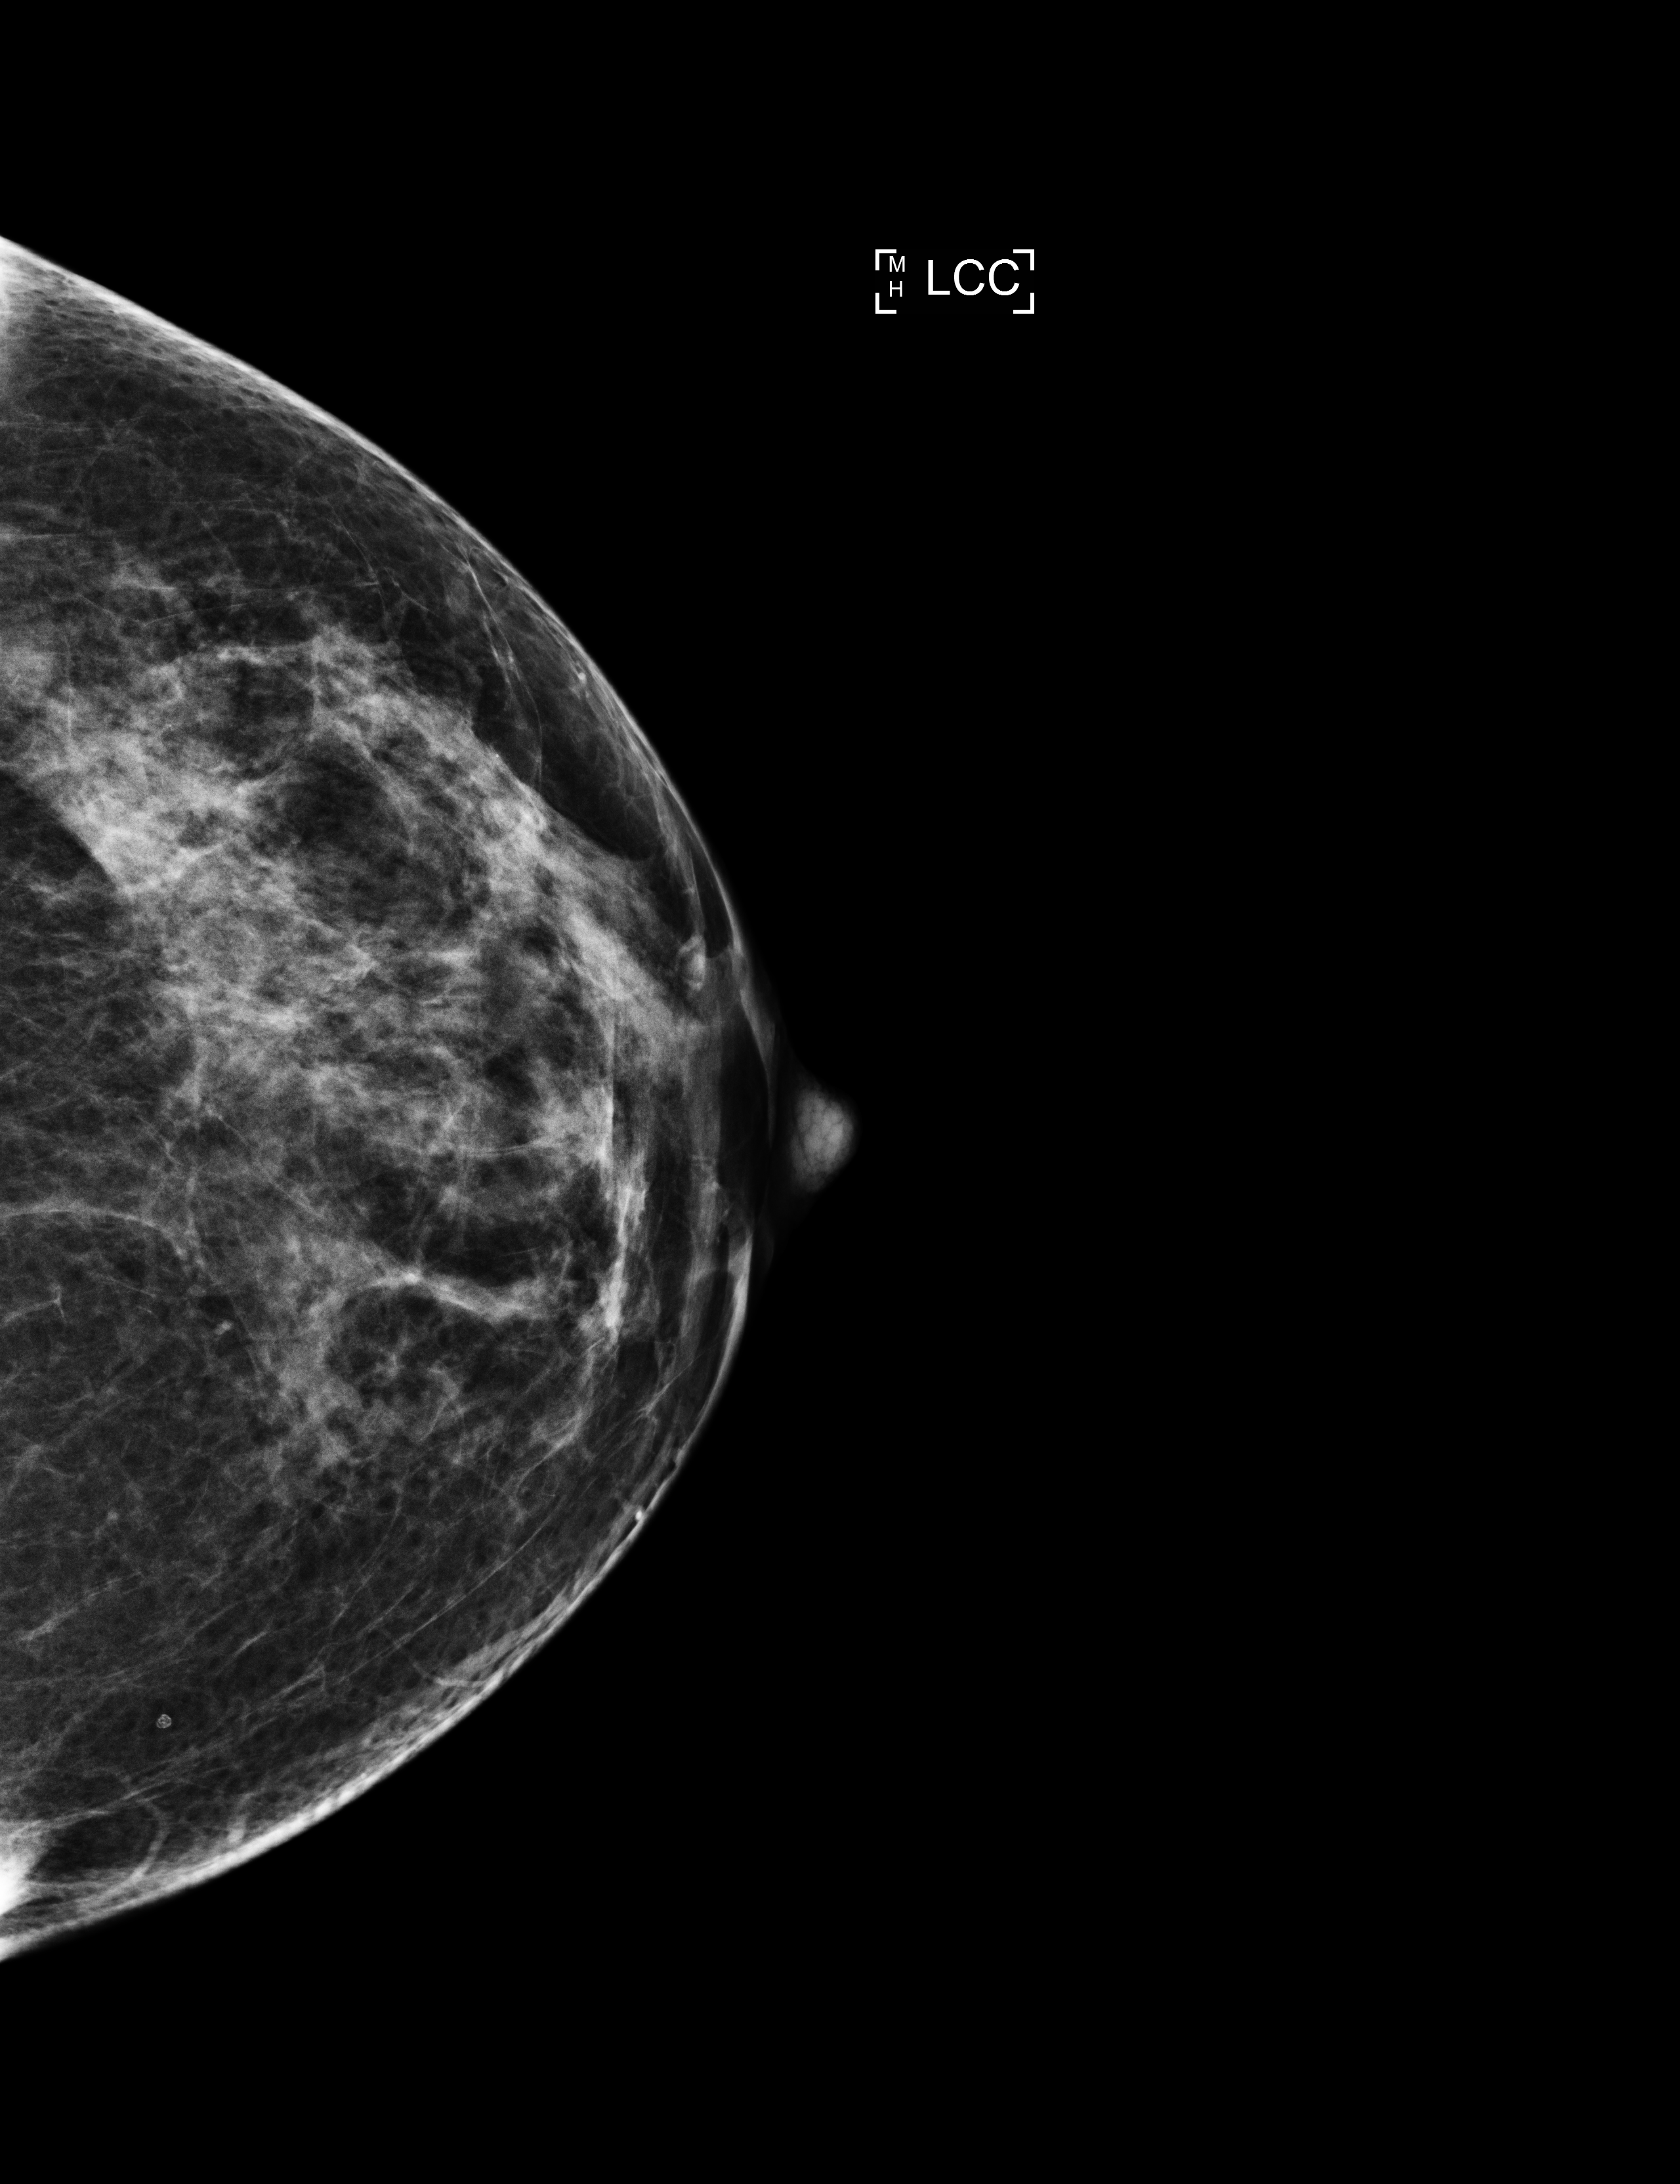
Digital mammogram (FFDM); left breast; cranio-caudal projection; annual screening mammography examination; compressed breast thickness 60 mm; system: Selenia Dimensions. Female patient, age 51 years.
Breast density at the screening exam (both breasts): heterogeneously dense (BI-RADS density category c). Final BI-RADS category for the screening round (tomosynthesis exam, both breasts): category 1. Recall: no recall after this screen.